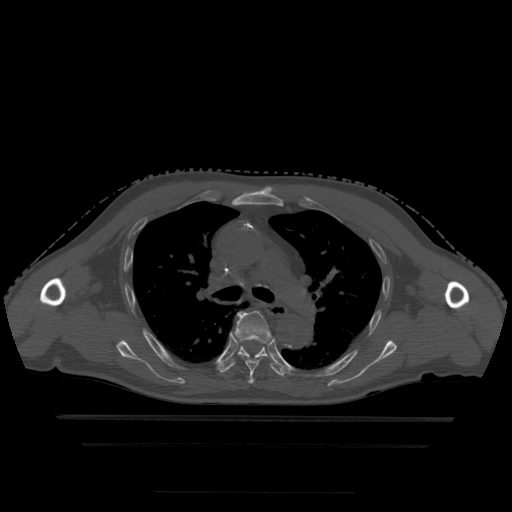
CT including the spine, one axial slice; position 329 of 522 along the scan axis; bone window (W 1800 / L 400 HU); 1.25 mm slice thickness; 512 × 512 image matrix. Patient age 68 years. Case-level facts recorded for this patient, not image findings: primary cancer: urothelial.
Annotated regions visible in this slice (semi-automatic segmentation, software-assisted and operator-edited):
- T5 vertebra: box from (x=235, y=311) to (x=271, y=384) px
- T6 vertebra: (x=218, y=338)–(x=286, y=377)